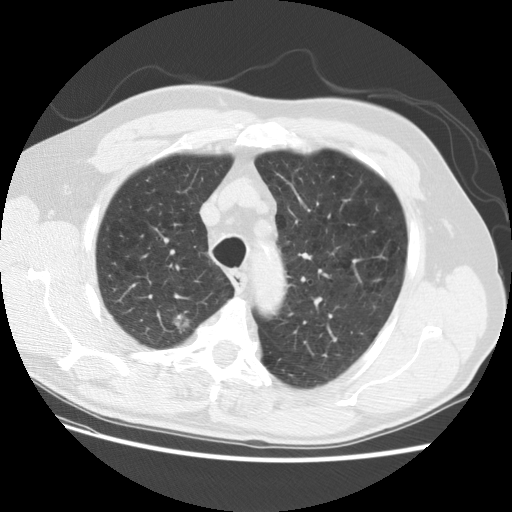
Low-dose screening chest CT, one axial slice; slice 98 of 124 in the series (ordered by position); reconstruction kernel STANDARD; 140 kVp; lung window (W 1500 / L -600 HU); 2.5 mm slice thickness; 512 × 512 image matrix, field of view 361 × 361 mm.
Outlined on this slice (expert manual segmentation):
- lesion 1 (tumor, upper lobe of right lung): bounding box (x1, y1, x2, y2) in pixels: (174, 314, 189, 333)